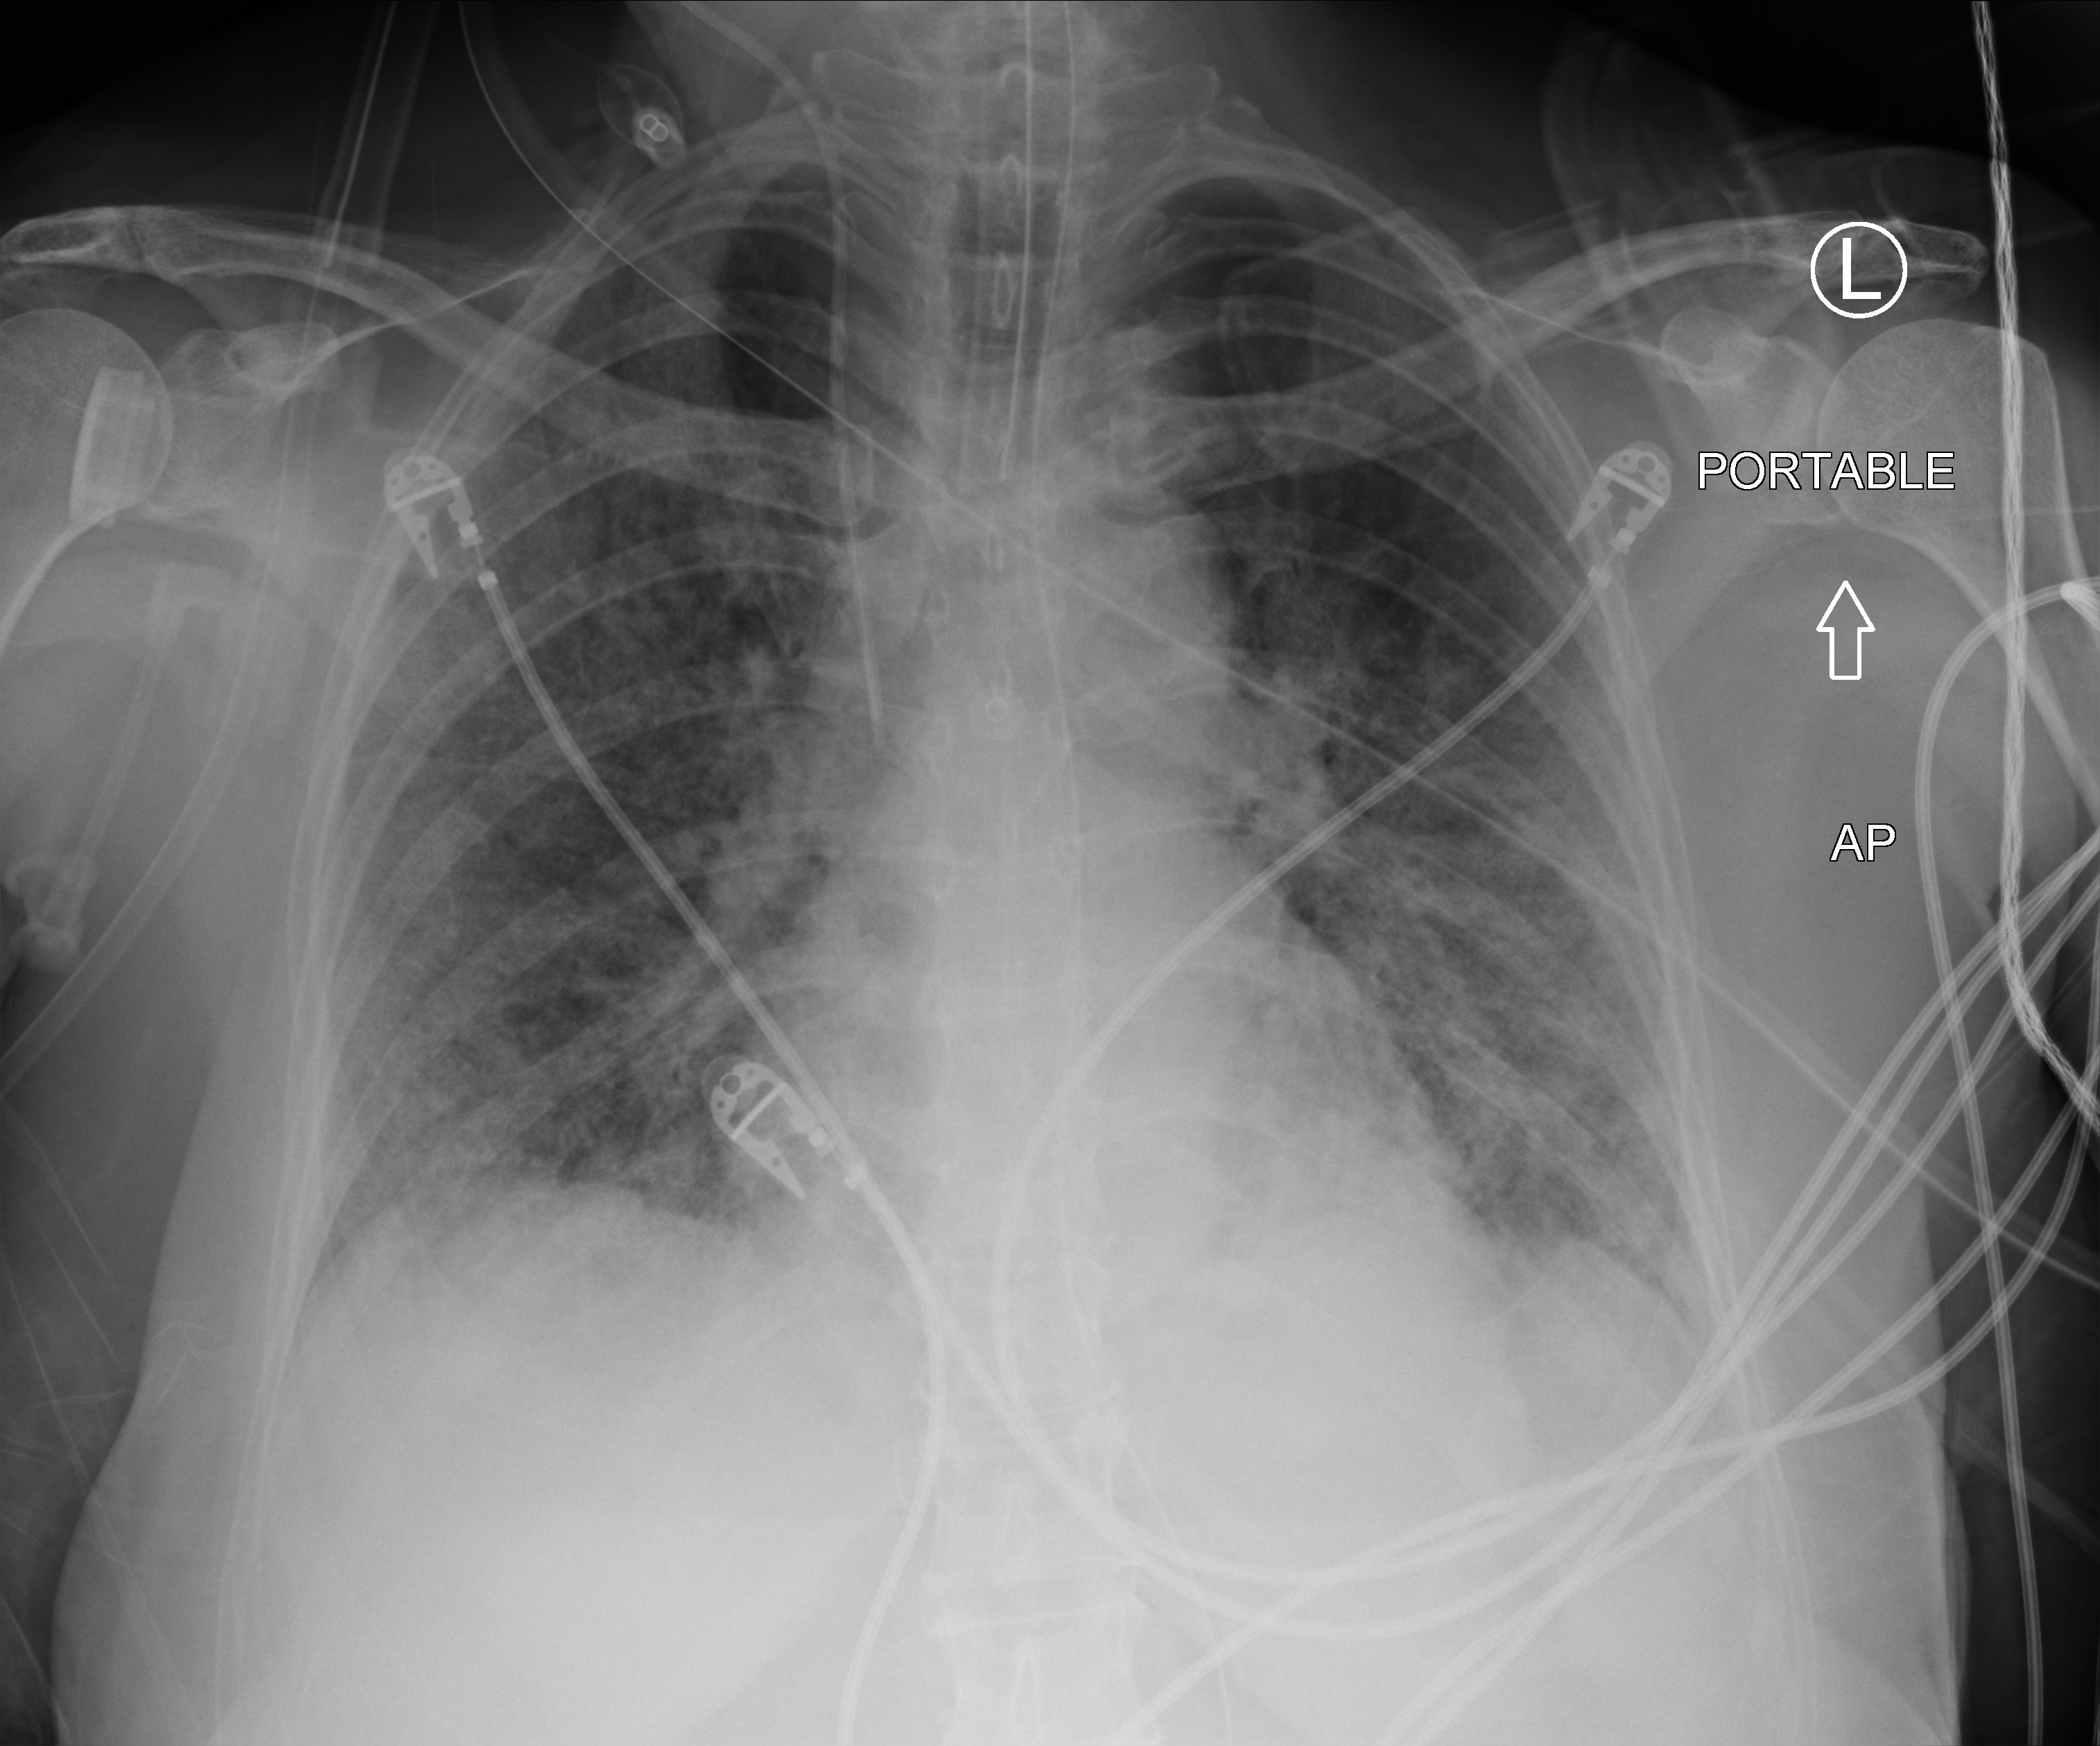
Portable chest radiograph, anteroposterior (AP) projection. Female patient hospitalised with COVID-19, age 60–74 years.
Hospital-stay facts (about this admission, not read from this image; timing relative to this image not recorded): chronic kidney disease (admission record): no; length of hospital stay: 43 days.